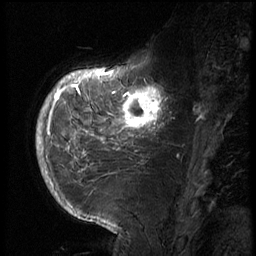
Breast MRI (dynamic contrast-enhanced), one sagittal slice. Slice 20 of 72 in the series (ordered by position). 3 images stored at this slice position (order not interpretable as contrast timing). 1.5 T. TE 4.2 ms, TR 8.9 ms. 256 × 256 image matrix, field of view 200 × 200 mm. Female patient, age 56 years. Case-level facts recorded for this patient, not image findings: setting: breast cancer imaged before/during neoadjuvant chemotherapy.
Outlined on this slice (semi-automatic segmentation, software-assisted and operator-edited):
- analysis volume of interest (the breast-tissue region the enhancement analysis was run in; not a lesion): bounding box (x1, y1, x2, y2) in pixels: (114, 76, 177, 138)
- tumour enhancement mask (voxels above the 140 % enhancement threshold inside the analysis volume of interest): (114, 85, 165, 132)